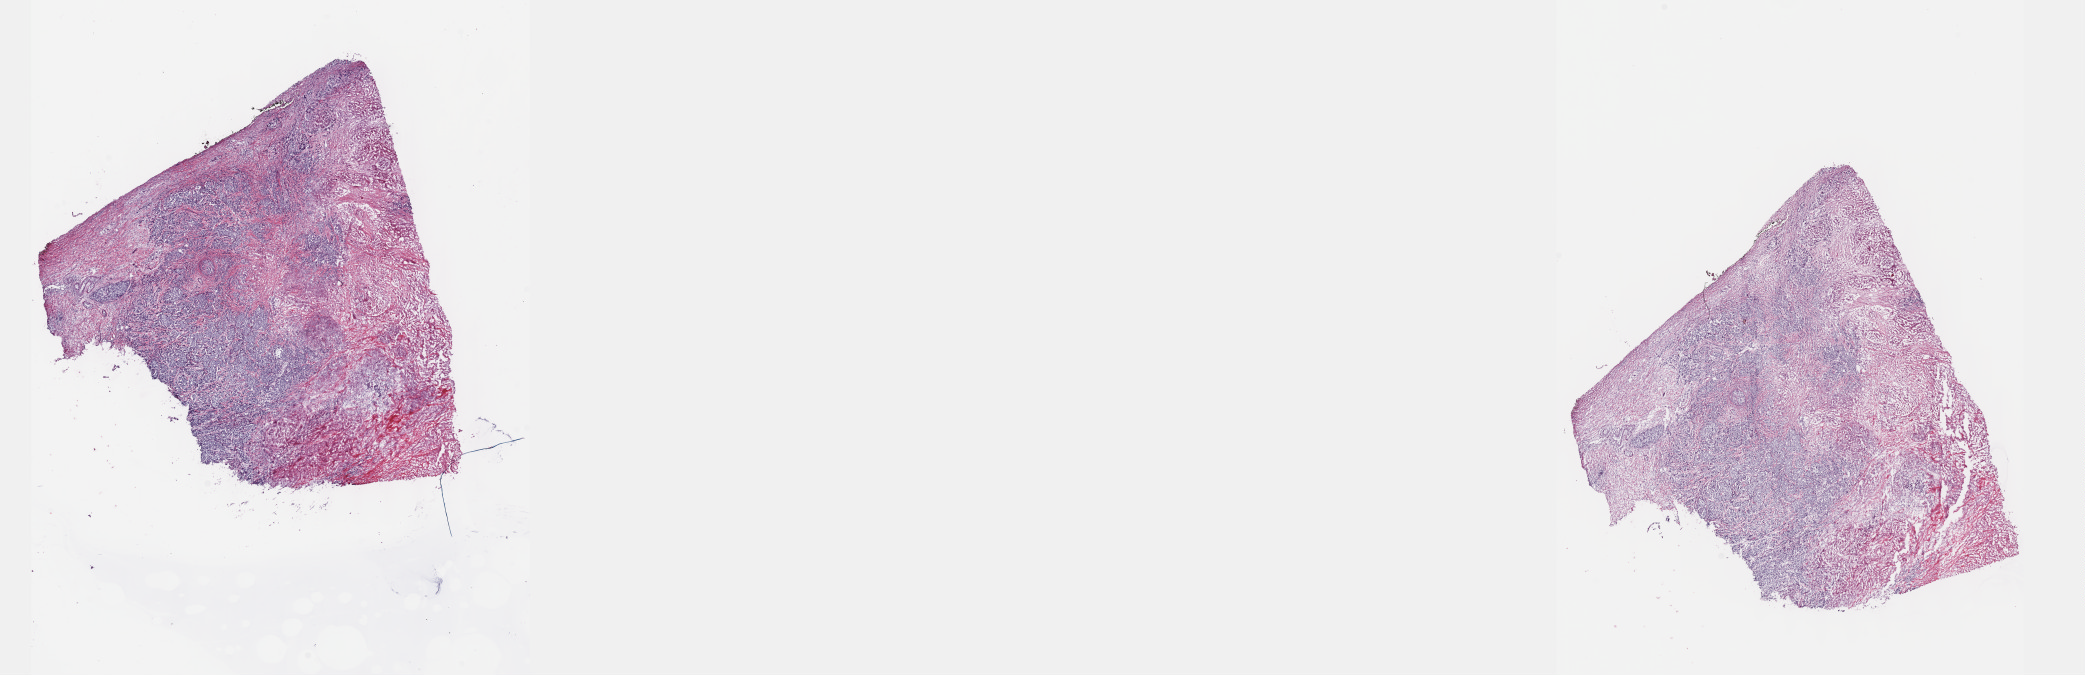
Whole-slide histology image, H&E-stained, whole scanned area (about 33.7 x 10.9 mm) shown as a low-resolution overview. Frozen section from the top of the tissue portion. Primary tumour sample from the pancreas. Patient: female, age at initial diagnosis 48 years. Histologic grade: G3 (poorly differentiated). Slide review estimates, as recorded: tumour cells 35%, tumour nuclei 85%, normal cells 0%, stromal cells 30%, necrosis 35%. Infiltration values recorded for this section: lymphocyte infiltration 5%, monocyte infiltration 2%, neutrophil infiltration 2%.
Lymph nodes positive (case pathology): 2 of 11 examined. AJCC pathologic stage: IIB (7th edition). Diagnosis: Infiltrating duct carcinoma, NOS (head of pancreas).